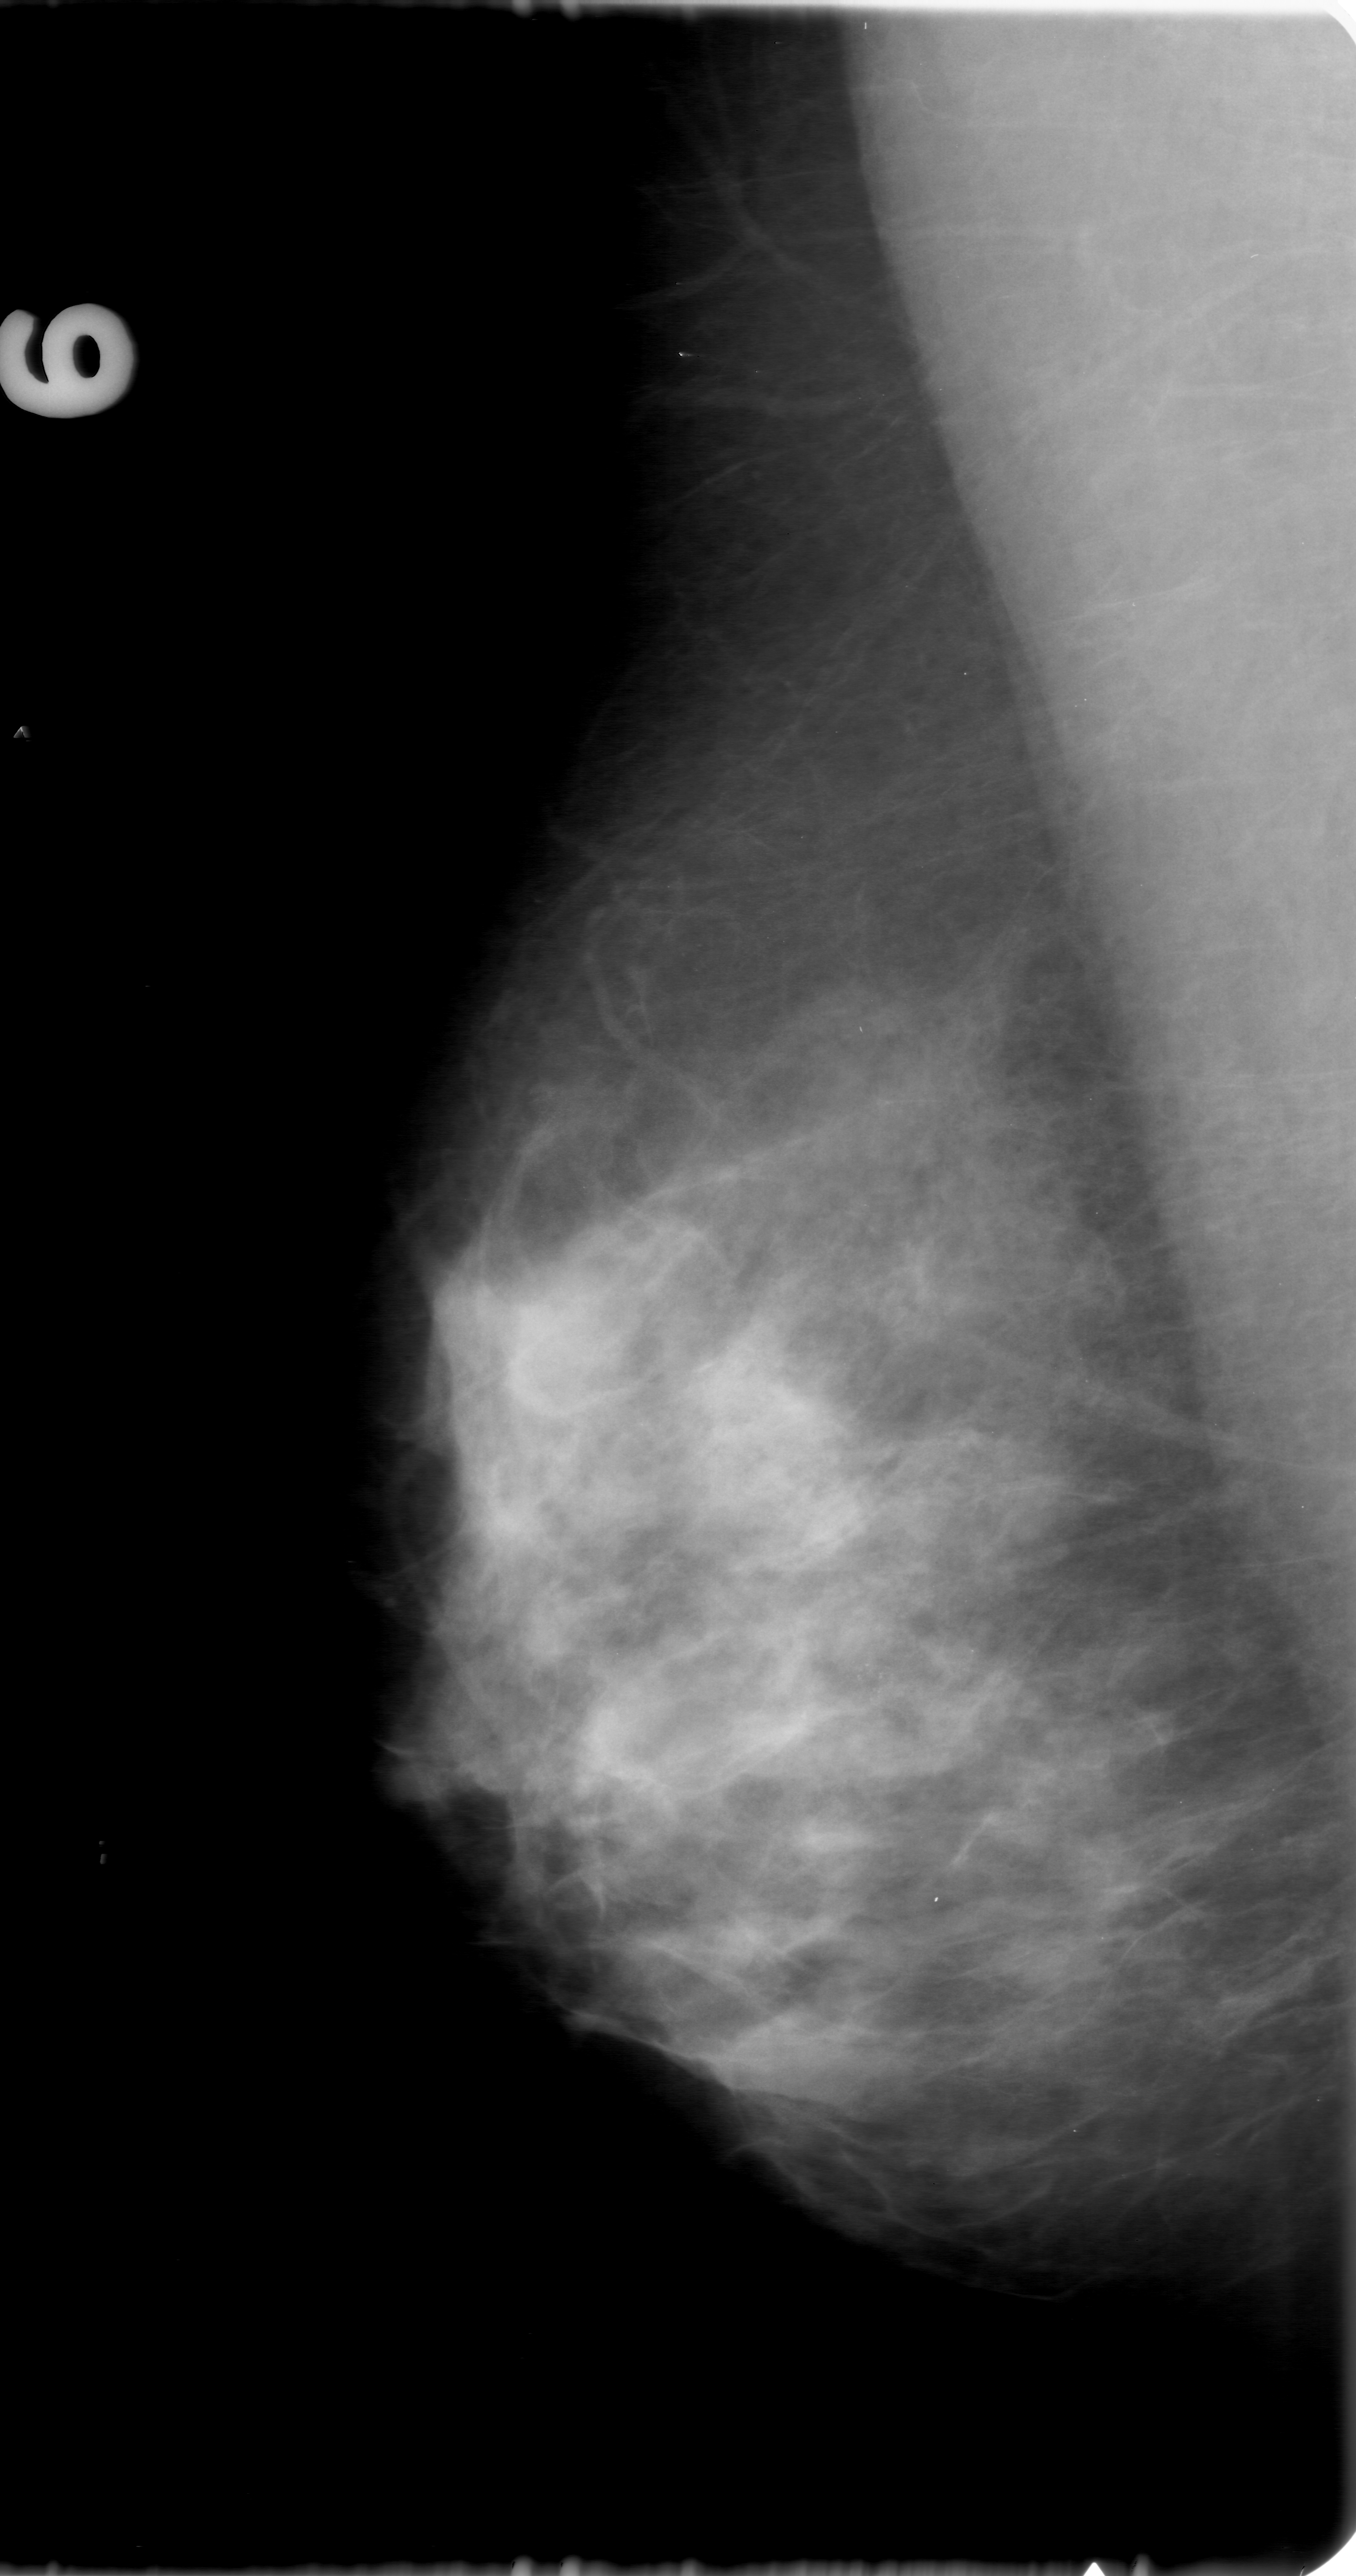
Mammogram (digitized film). Right breast. MLO view. Breast composition: heterogeneously dense (BI-RADS density category 3 of 4). 1356 × 2576 image matrix.
Expert-marked regions of interest on this image (one box per marked abnormality):
- calcifications, morphology amorphous, distribution clustered; BI-RADS assessment category 3; subtlety rating 3 on a 1 (subtle) to 5 (obvious) scale; pathology result (as recorded, not read from the image): malignant: box from (x=736, y=1575) to (x=1043, y=1819) px